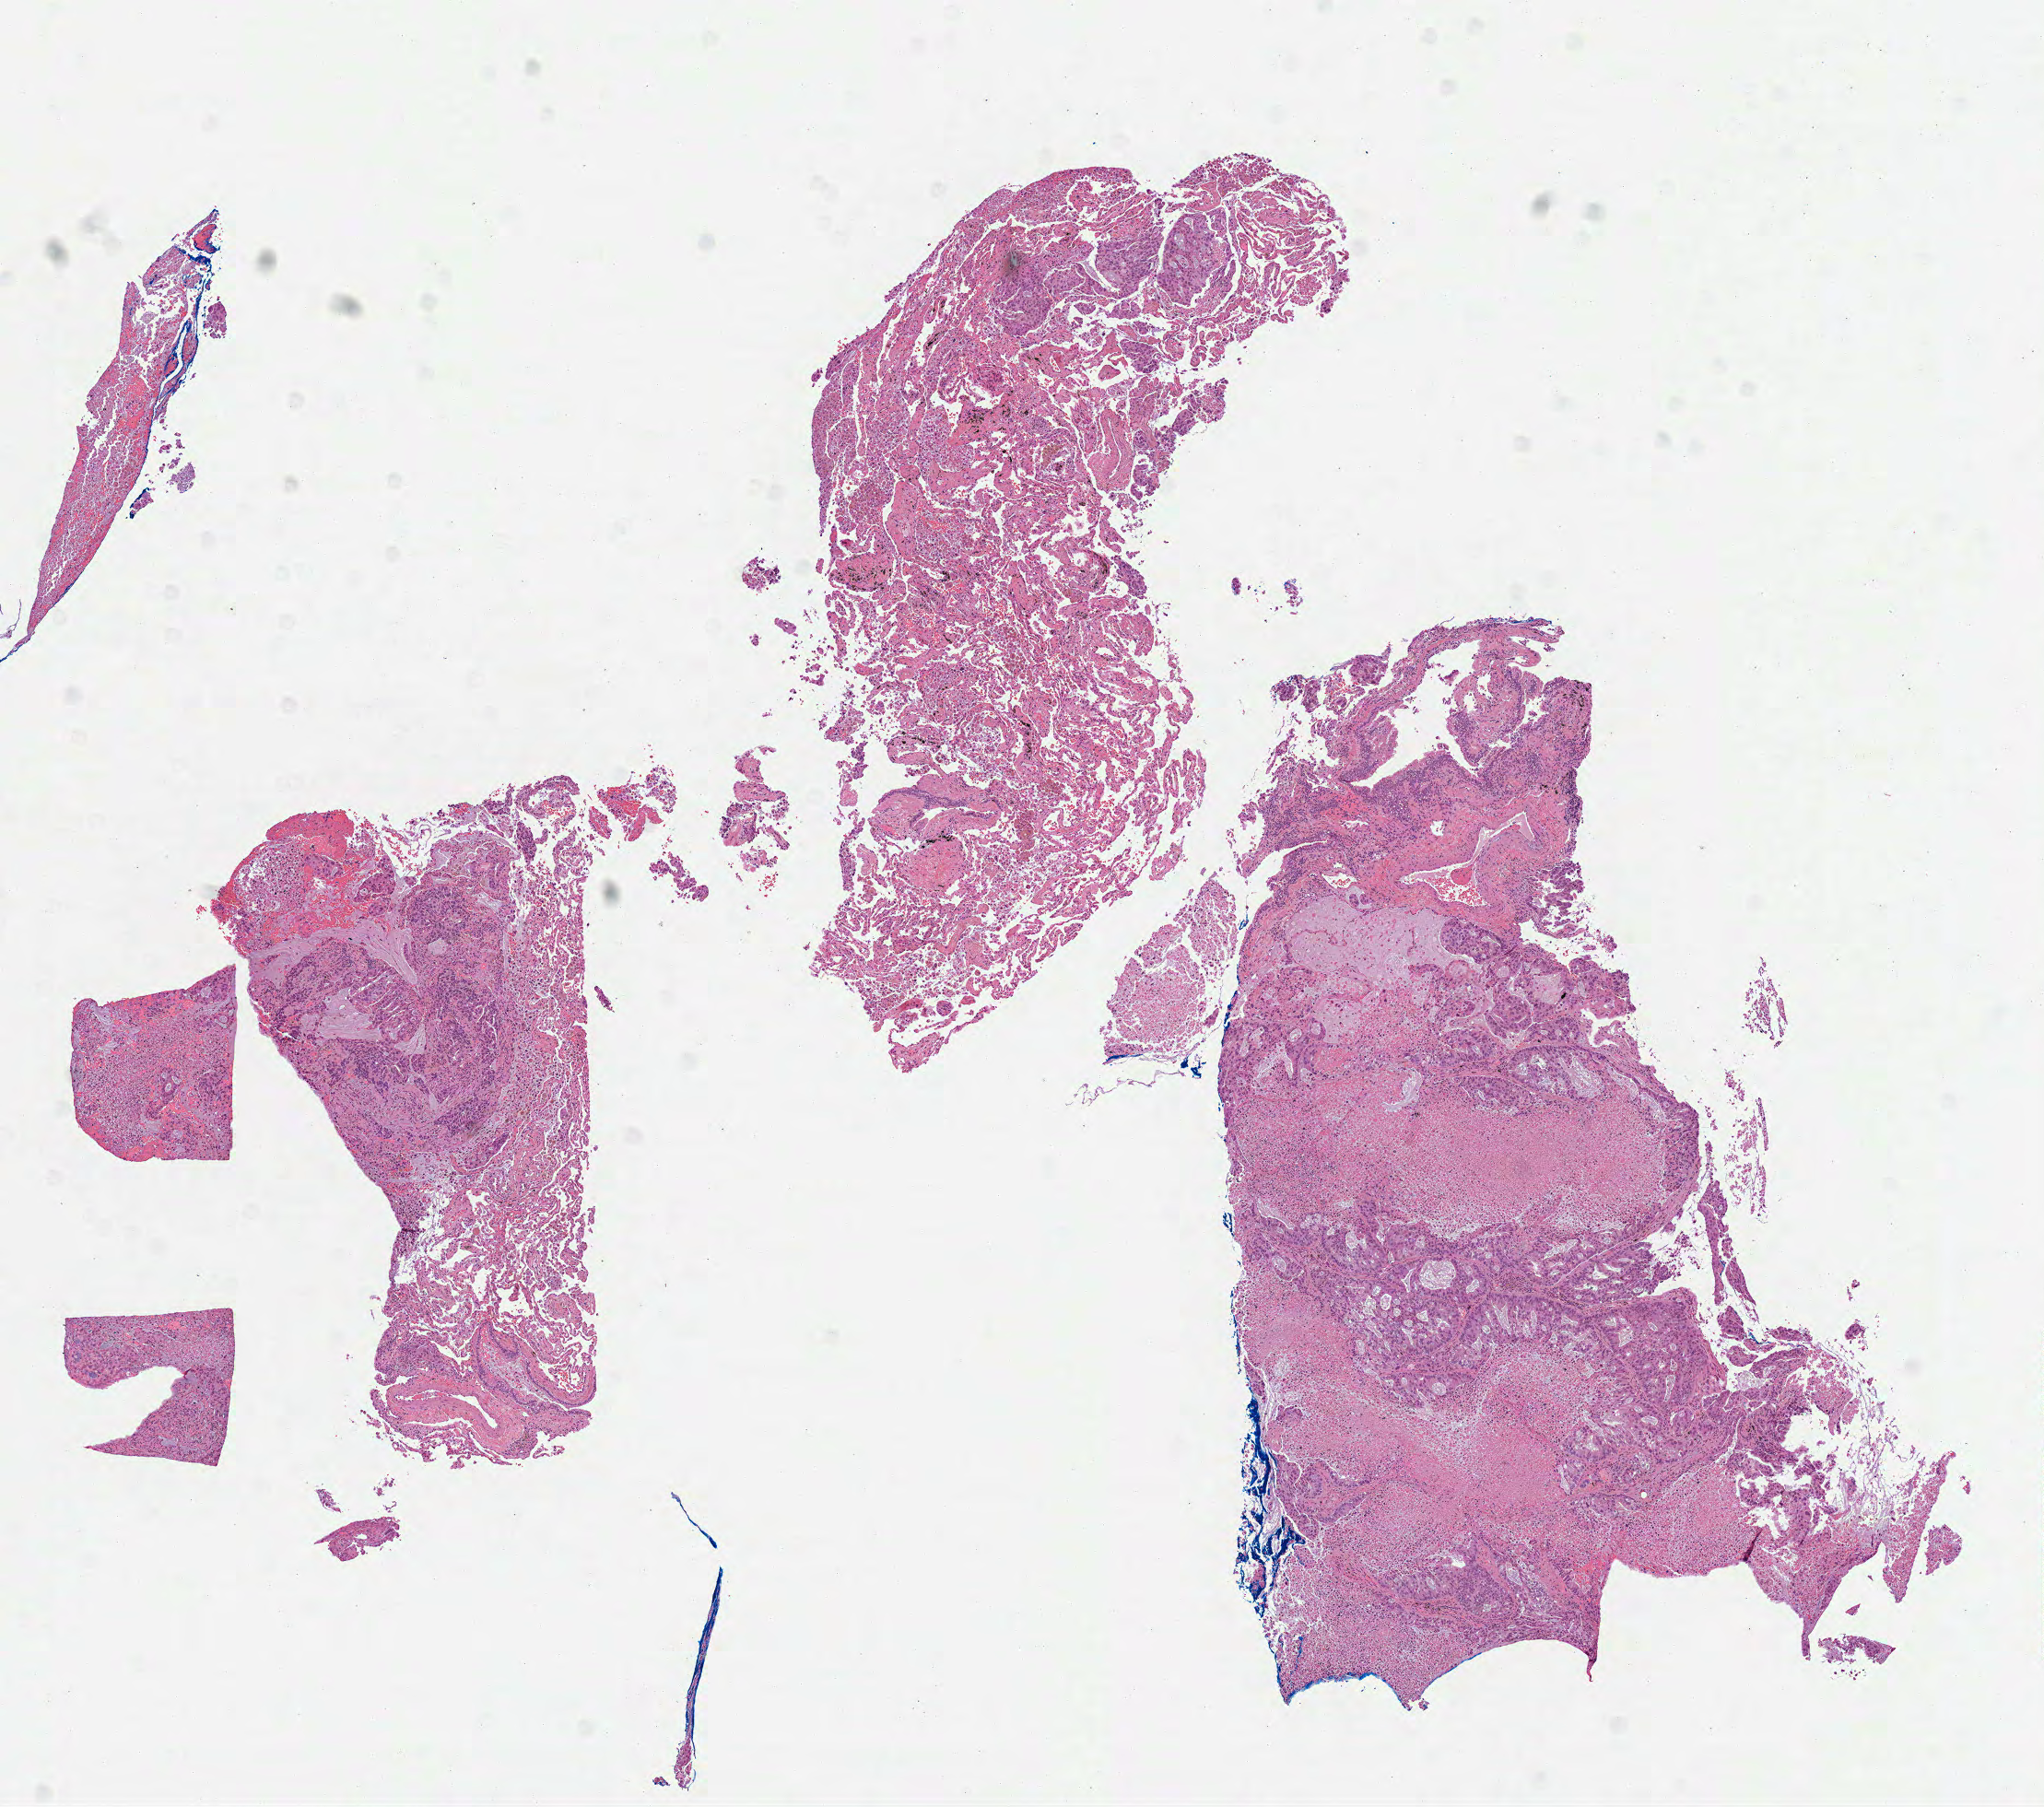
Whole-slide histology image, H&E-stained — whole scanned area (about 8.9 x 7.9 mm, slide scanned at 40x) shown as a low-resolution overview; formalin-fixed paraffin-embedded (FFPE) diagnostic section; sample: primary tumour, lung. Patient: male, age at initial diagnosis 51 years.
* laterality: left
* AJCC pathologic stage: IV (7th edition)
* diagnosis: Adenocarcinoma, NOS (upper lobe, lung)